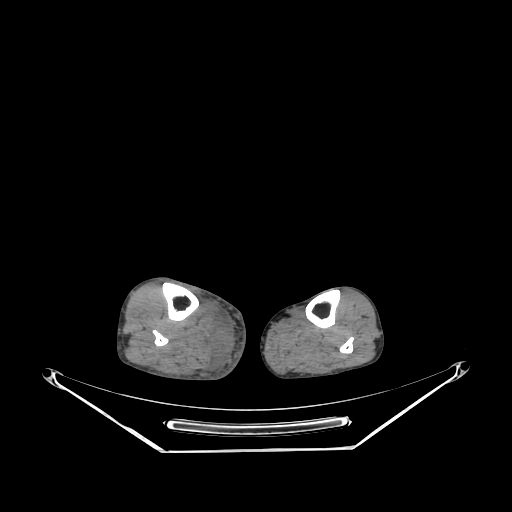
CT of an extremity soft-tissue mass (from a PET/CT study), one axial slice. Slice 124 of 267 in the series (ordered by position). Reconstruction kernel SOFT. 140 kVp. Soft-tissue window (W 400 / L 40 HU). 3.75 mm slice thickness. 512 × 512 image matrix, field of view 500 × 500 mm. Male patient. Case-level facts recorded for this patient, not image findings: histological type: pleiomorphic liposarcoma; grade: high; site of the primary tumour: right calf.
Annotated regions visible in this slice (expert contour drawn on MRI and transferred to this co-registered scan by the dataset authors):
- gross tumour volume including surrounding oedema: box from (x=206, y=317) to (x=234, y=359) px
- gross tumour volume (mass): (x=221, y=336)–(x=223, y=339)